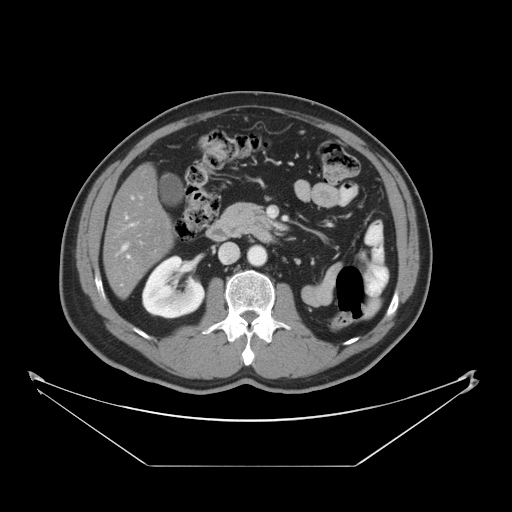
Contrast-enhanced abdominal CT, one axial slice; 120 kVp; intravenous contrast given; soft-tissue window (W 400 / L 40 HU); 5 mm slice thickness; 512 × 512 image matrix. Male patient, age 57 years. From the clinical record (not read from this slice): diagnosis: colorectal cancer liver metastases, imaged before liver resection; multiple liver metastases: no; largest metastasis: 3.3 cm; chemotherapy before resection: yes.
Annotated regions visible in this slice (manually delineated by an expert):
- hepatic veins: bounding box <123,245,127,249> (left, top, right, bottom; pixels)
- liver: <105,166,173,297>
- planned liver remnant (the part of the liver to remain after resection): <105,166,173,297>
- portal vein (with intrahepatic branches): <127,255,130,258>